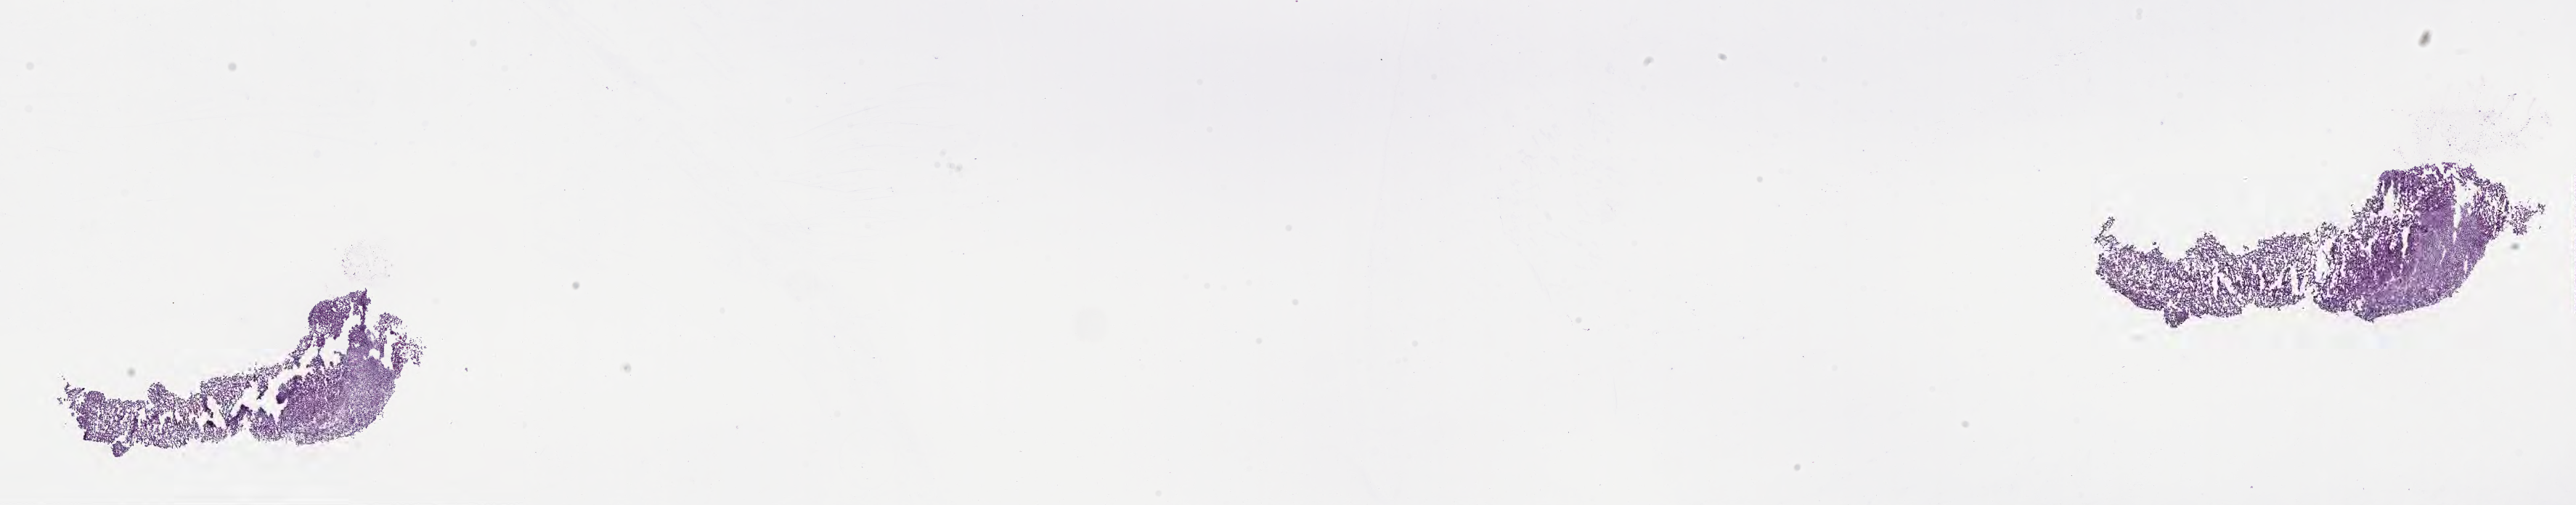
Digitized hematoxylin and eosin (H&E)-stained section of tumor tissue from the frontal lobe — shown as a low-resolution overview of the whole scanned area (about 28.7 x 5.6 mm), frozen section (OCT-embedded). Patient female; age 217 months (18 years 1 month).
Diagnosis: Glioma, malignant.